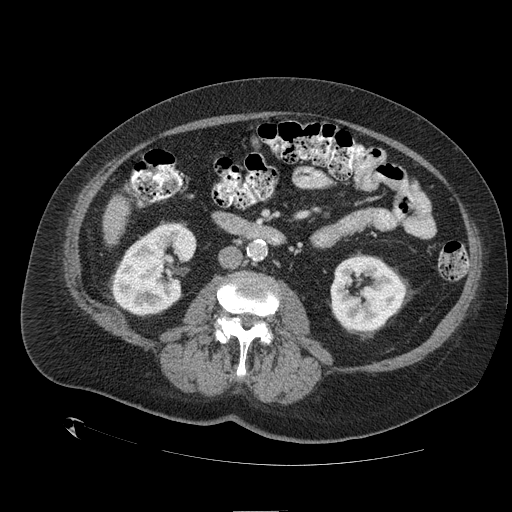
Contrast-enhanced abdominal CT (liver protocol), one axial slice; position 34 of 109 along the scan axis; reconstruction kernel STANDARD; 120 kVp; one of 2 acquisitions stored at this slice position; soft-tissue window (W 400 / L 40 HU); 2.5 mm slice thickness; 512 × 512 image matrix. Case-level facts recorded for this patient, not image findings: diagnosis: hepatocellular carcinoma (patient treated with transarterial chemoembolisation; whether this scan precedes or follows treatment is not stated here); TNM stage (as recorded): Stage-I; Child-Pugh class: A.
Structures marked on this image (semi-automatic segmentation, software-assisted and operator-edited):
- liver parenchyma outside the tumour (the mass and vessels are separate outlines, so this box may not span the whole liver): bounding box <102,196,128,244> (left, top, right, bottom; pixels)